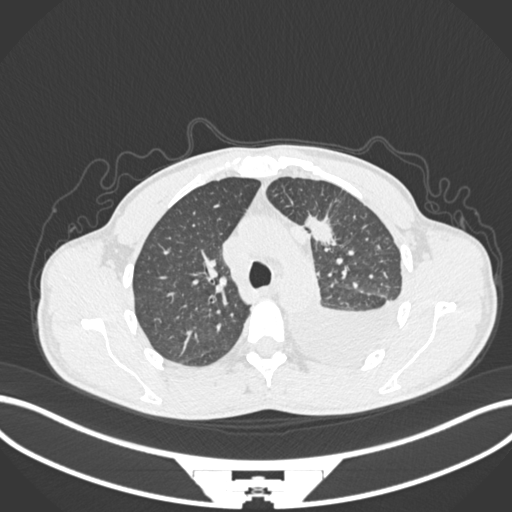
Chest CT, one axial slice. Position 155 of 244 along the scan axis. 120 kVp. Lung window (W 1500 / L -600 HU). 512 × 512 image matrix. Patient: male, 49 years. From the clinical record (not read from this slice): clinical TNM (as recorded): T1c N1 M1.
Structures marked on this image (rectangle marked by the reading radiologist):
- lung tumour (recorded histology: adenocarcinoma): box from (x=305, y=206) to (x=340, y=250) px